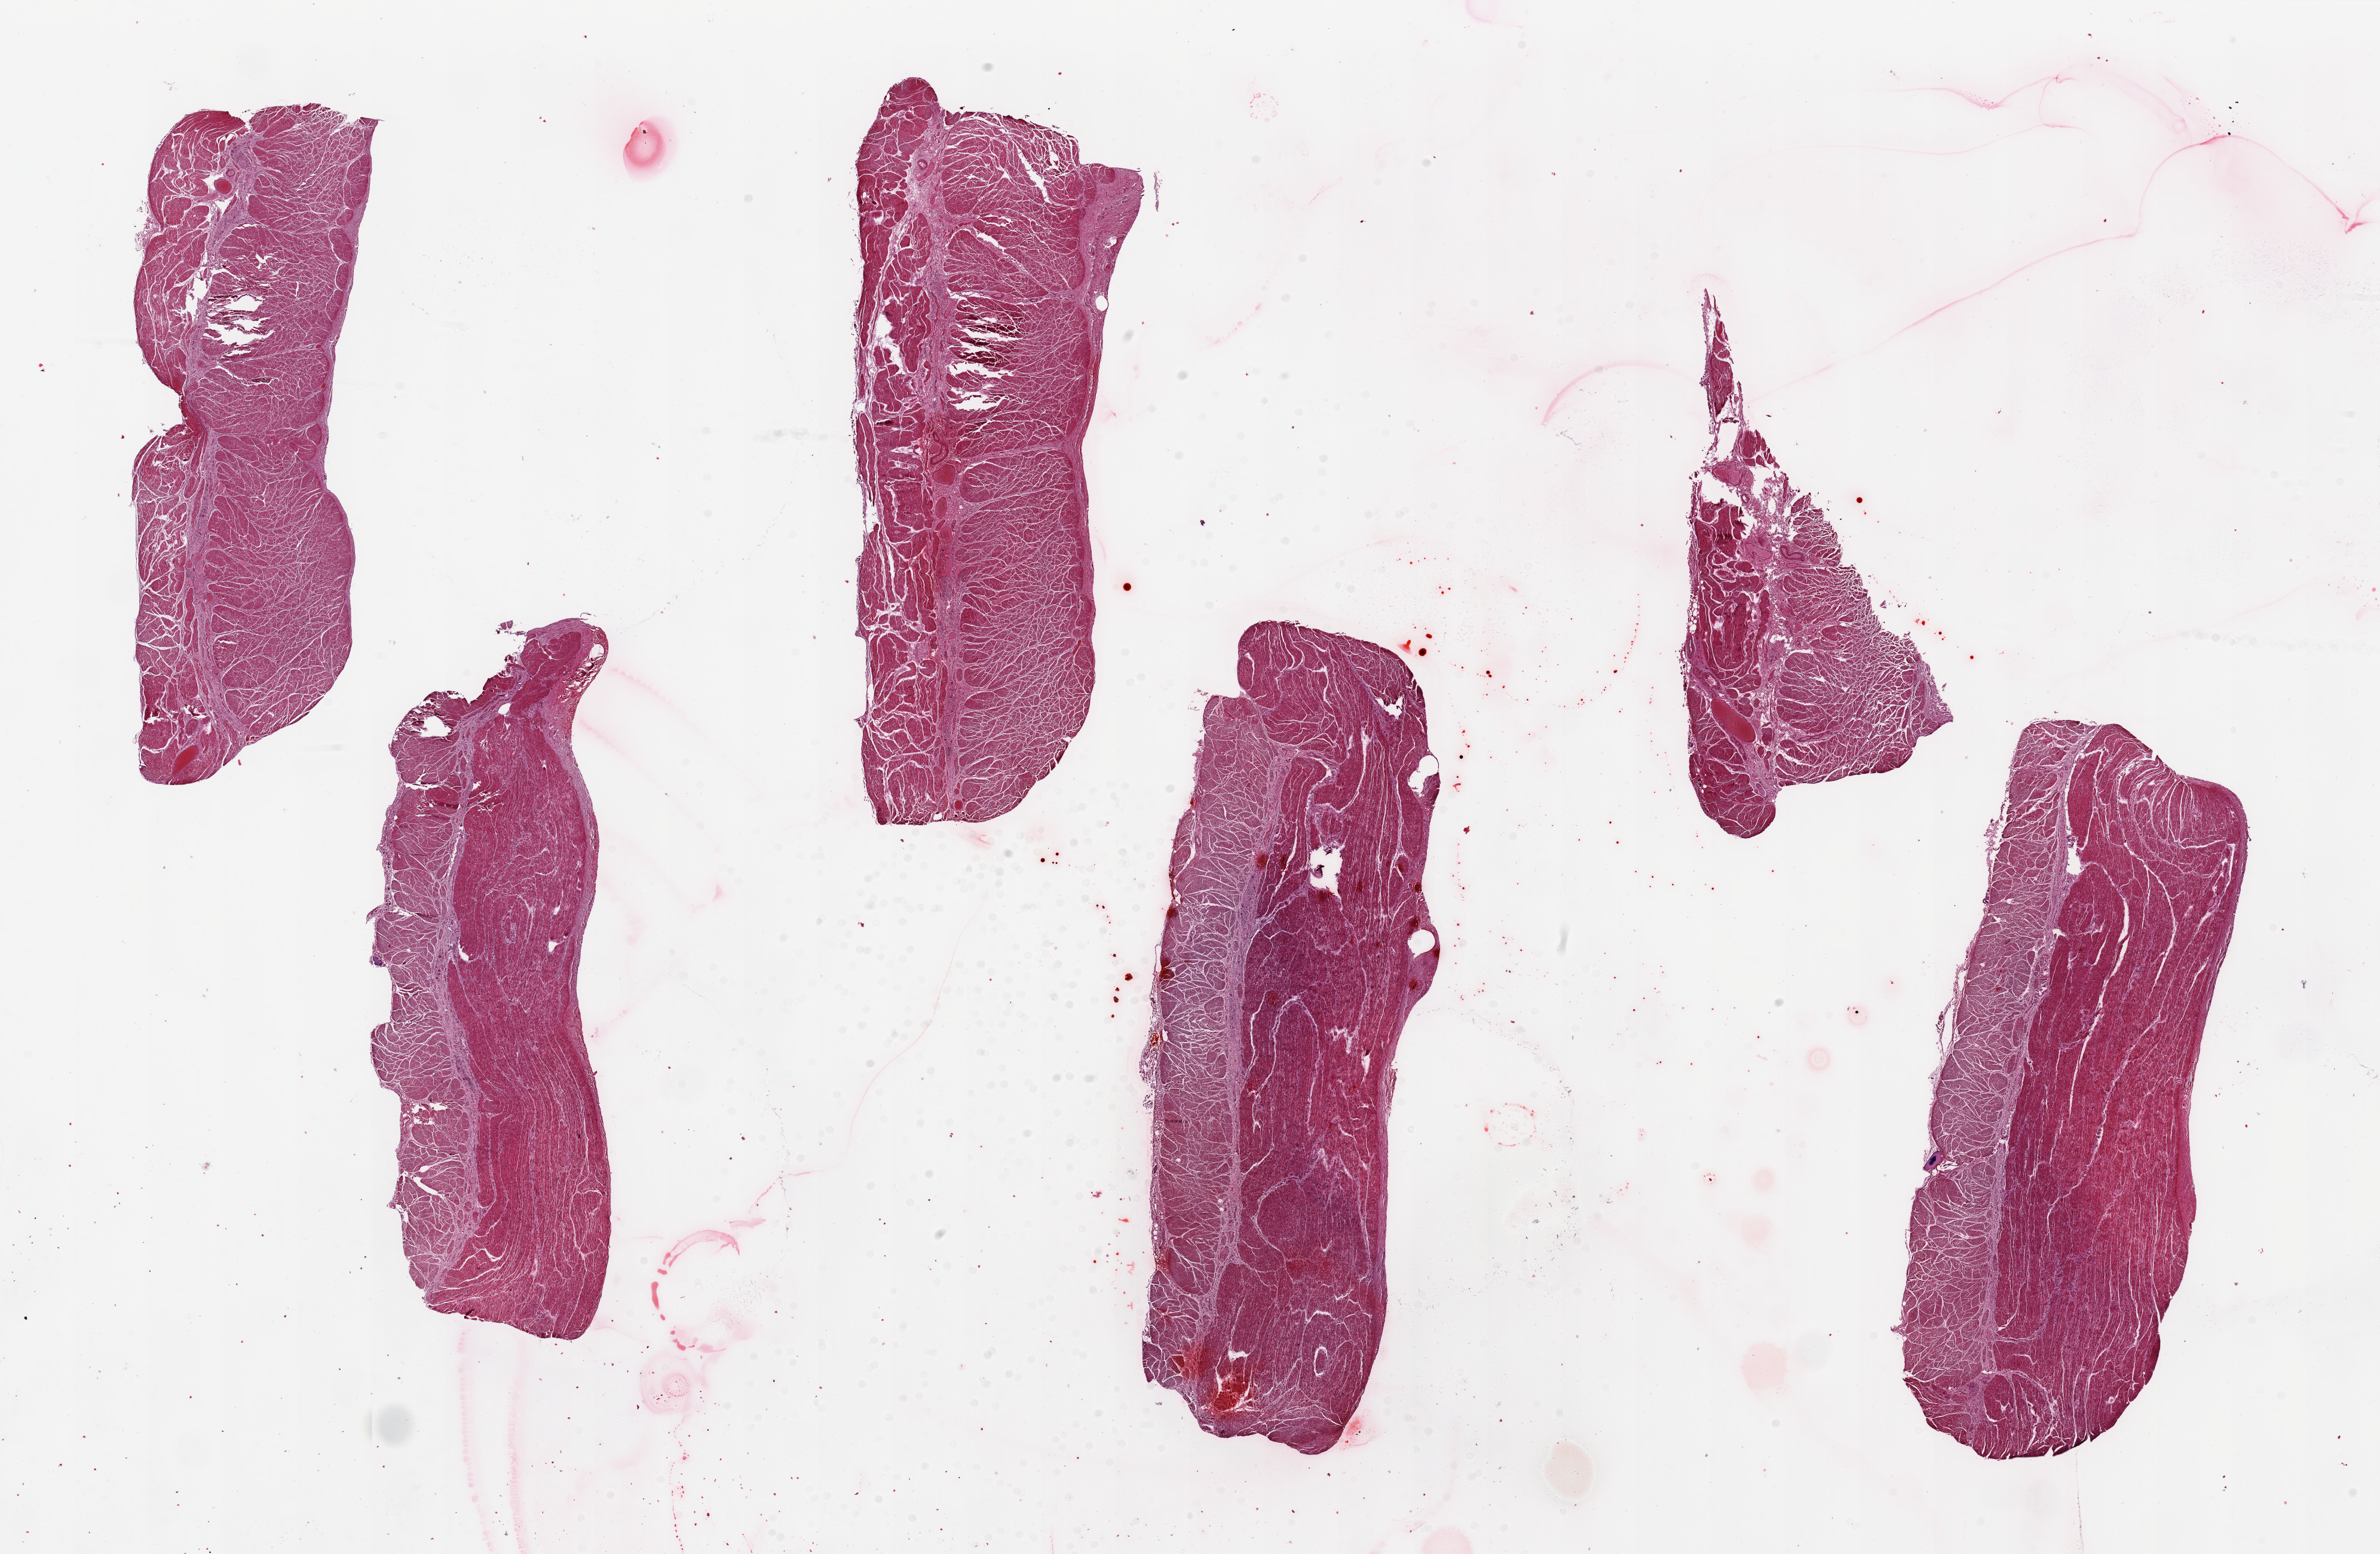
Whole-slide image, hematoxylin and eosin (H&E) stain, whole scanned area (about 31.5 x 20.6 mm) shown as a low-resolution overview; PAXgene-fixed, paraffin-embedded tissue; target tissue: esophageal muscle; donor tissue sample. Donor: male.
* reviewer comment on this tissue sample: 6 pieces, up to 11x4mm